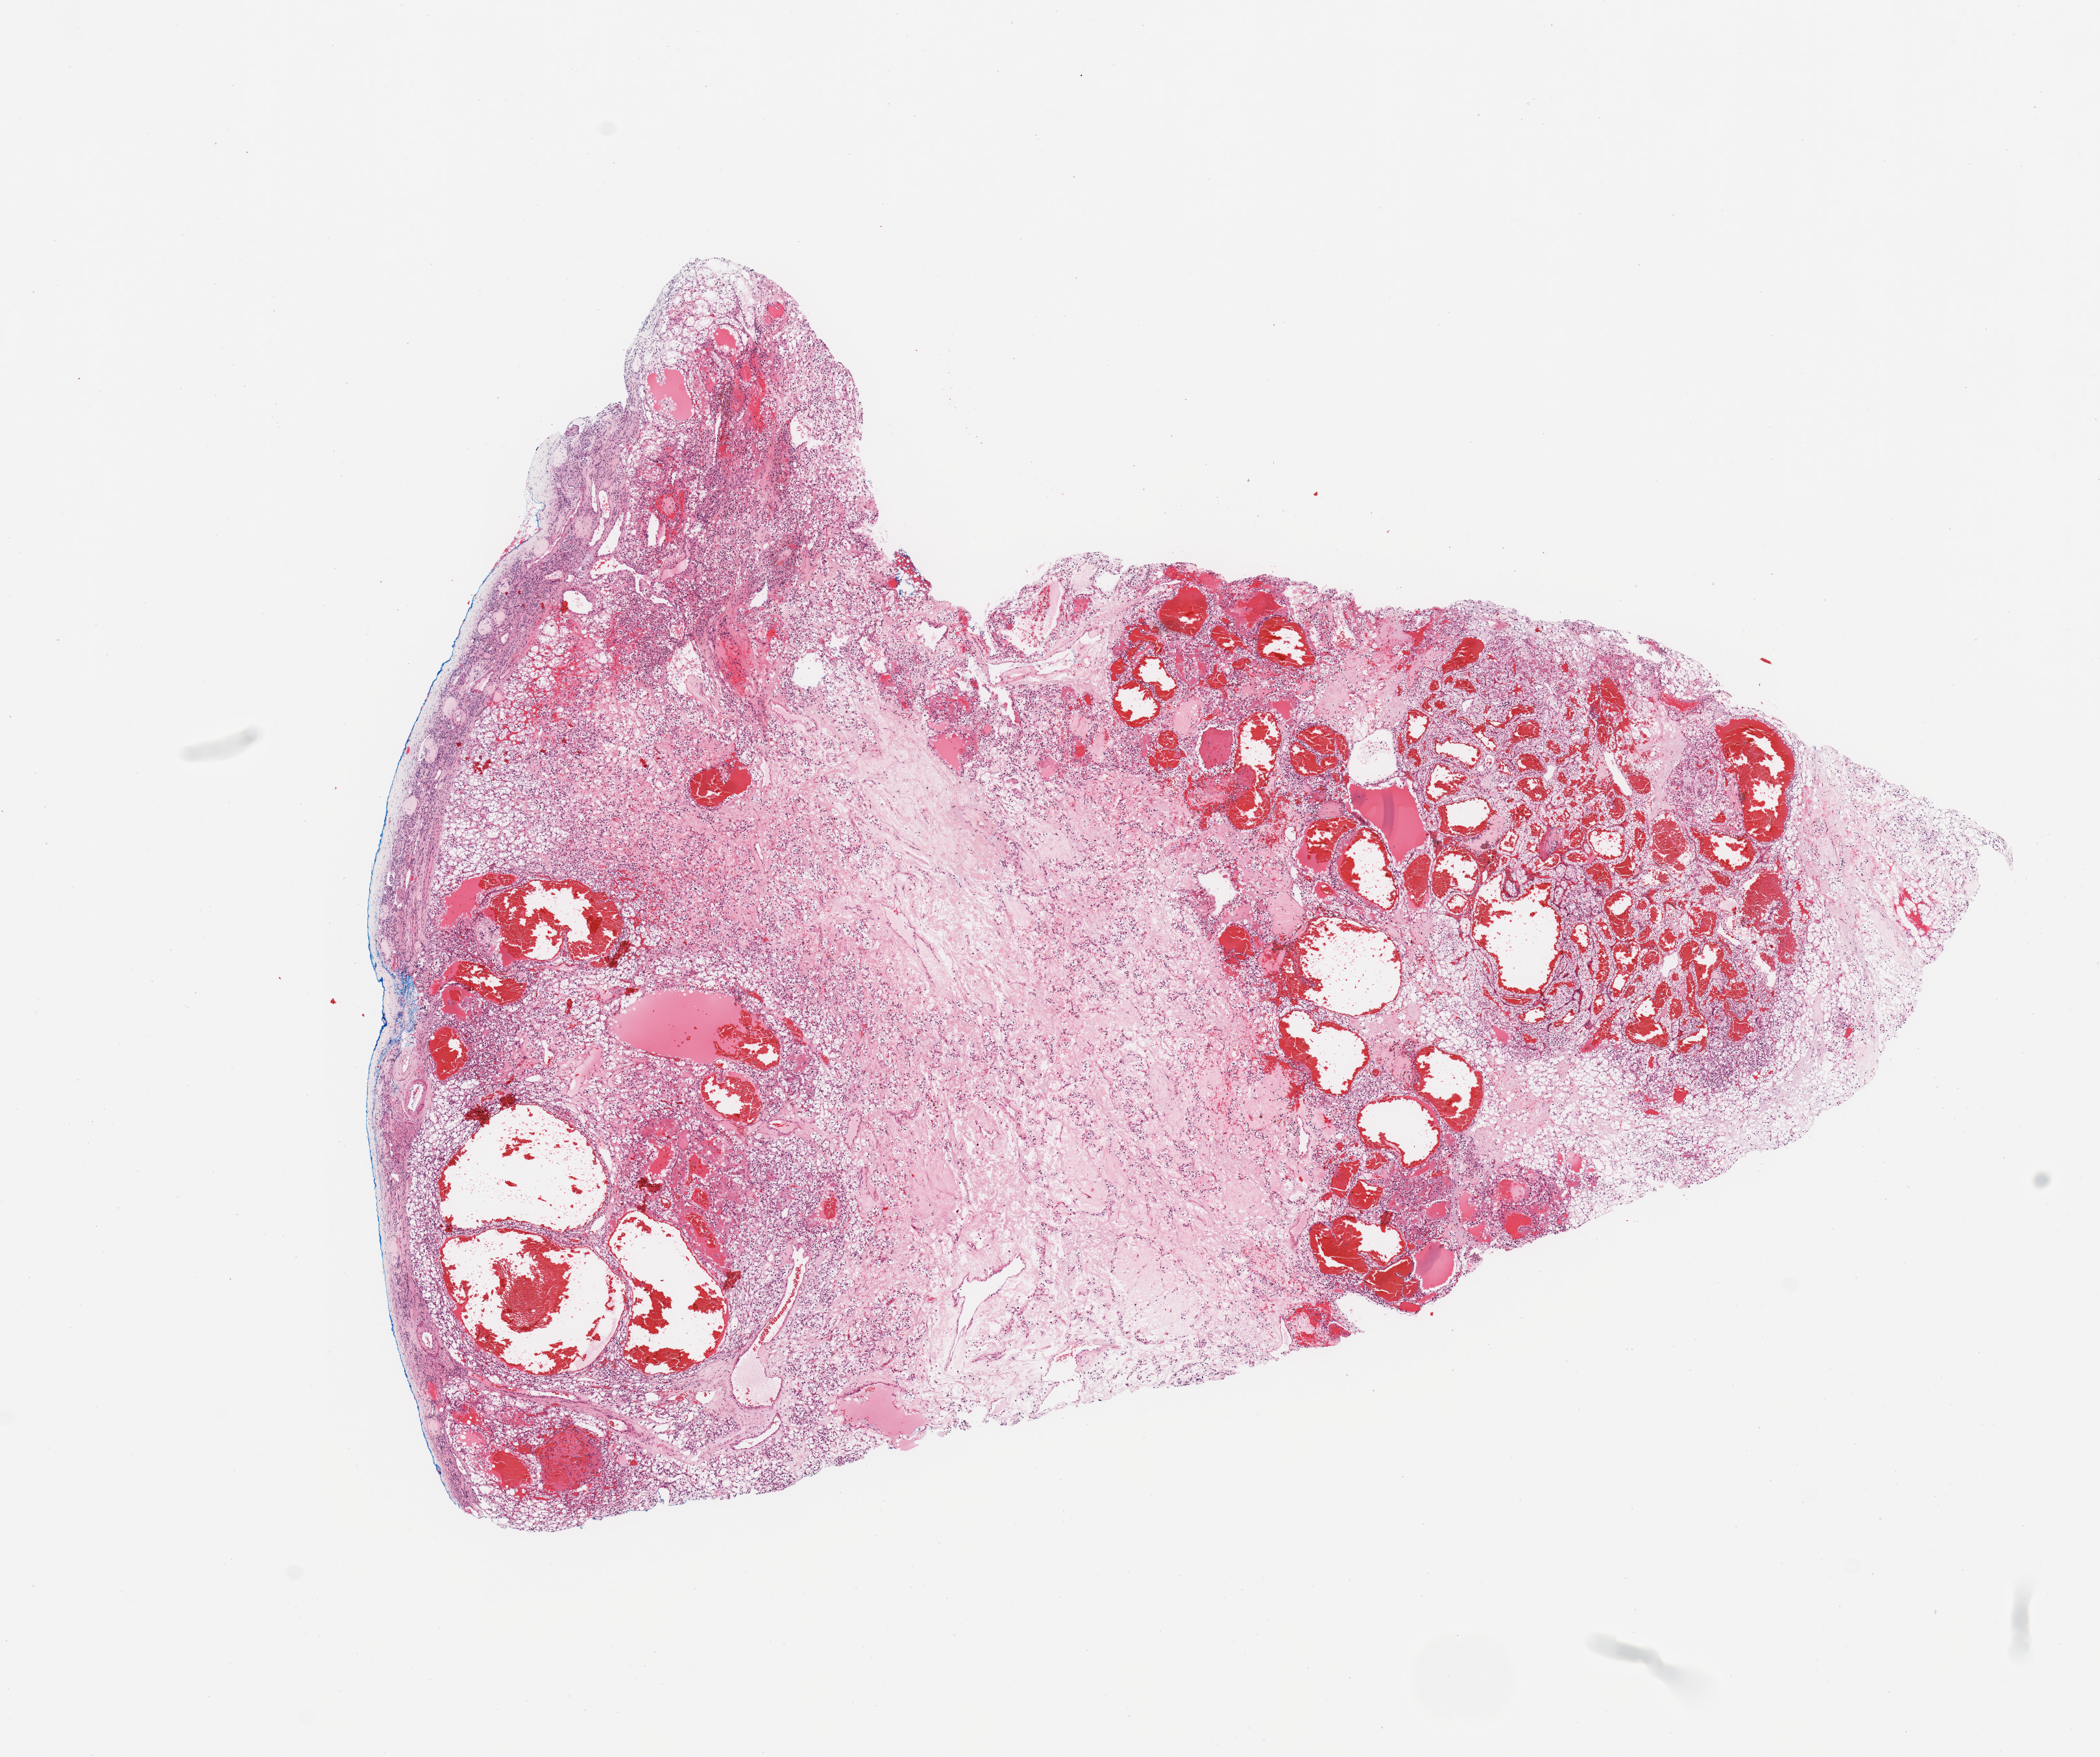
Hematoxylin and eosin (H&E) stained whole-slide image — low-resolution overview of the scanned area, about 12.8 x 10.7 mm, tumour tissue sample, sampled site: kidney. 69-year-old female patient.
Diagnosis: Renal cell carcinoma, NOS.